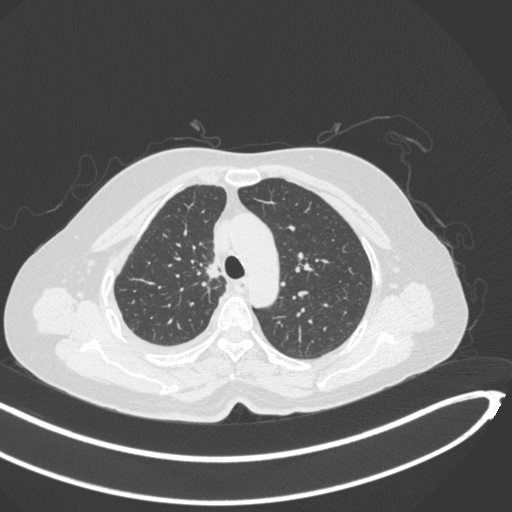
Chest CT, one axial slice. Position 226 of 297 along the scan axis. Reconstruction kernel B31f. 120 kVp. Lung window (W 1500 / L -600 HU). 1 mm slice thickness. 512 × 512 image matrix, field of view 400 × 400 mm. Female patient, age 64 years. Case-level facts recorded for this patient, not image findings: clinical TNM (as recorded): T1b N0 M1.
Outlined on this slice (rectangle marked by the reading radiologist):
- lung tumour (recorded histology: adenocarcinoma): bounding box [x1, y1, x2, y2] px = [205, 260, 226, 282]